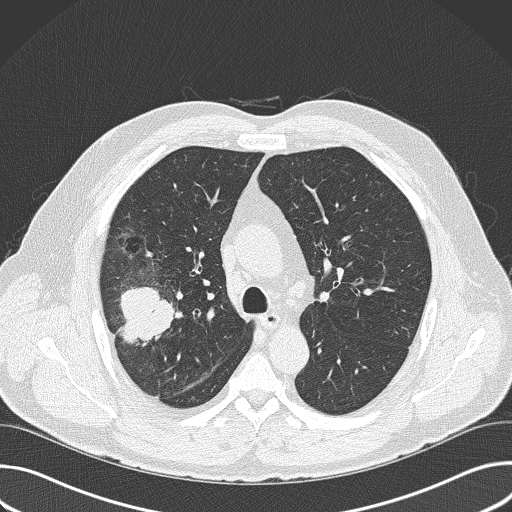
Low-dose screening chest CT, axial slice. Baseline annual screen. Lung window (W 1500 / L -600 HU). 2 mm slice thickness. Male participant, aged 56 years at enrolment. Current smoker at enrolment.
- Lesion marked by an expert reader, box from (x=83, y=266) to (x=188, y=376) px.
- The exam's reader record, not a measurement of the box and not confirmed to be the same lesion: non-calcified nodule or mass ≥4 mm, right upper lobe, 6 × 5 mm, spiculated (stellate) margins, soft tissue attenuation.
- Lung cancer was diagnosed 16 days after this screen: adenocarcinoma, NOS, right upper lobe, poorly differentiated (G3), stage IIB (AJCC 6th edition), 60 mm at pathology.